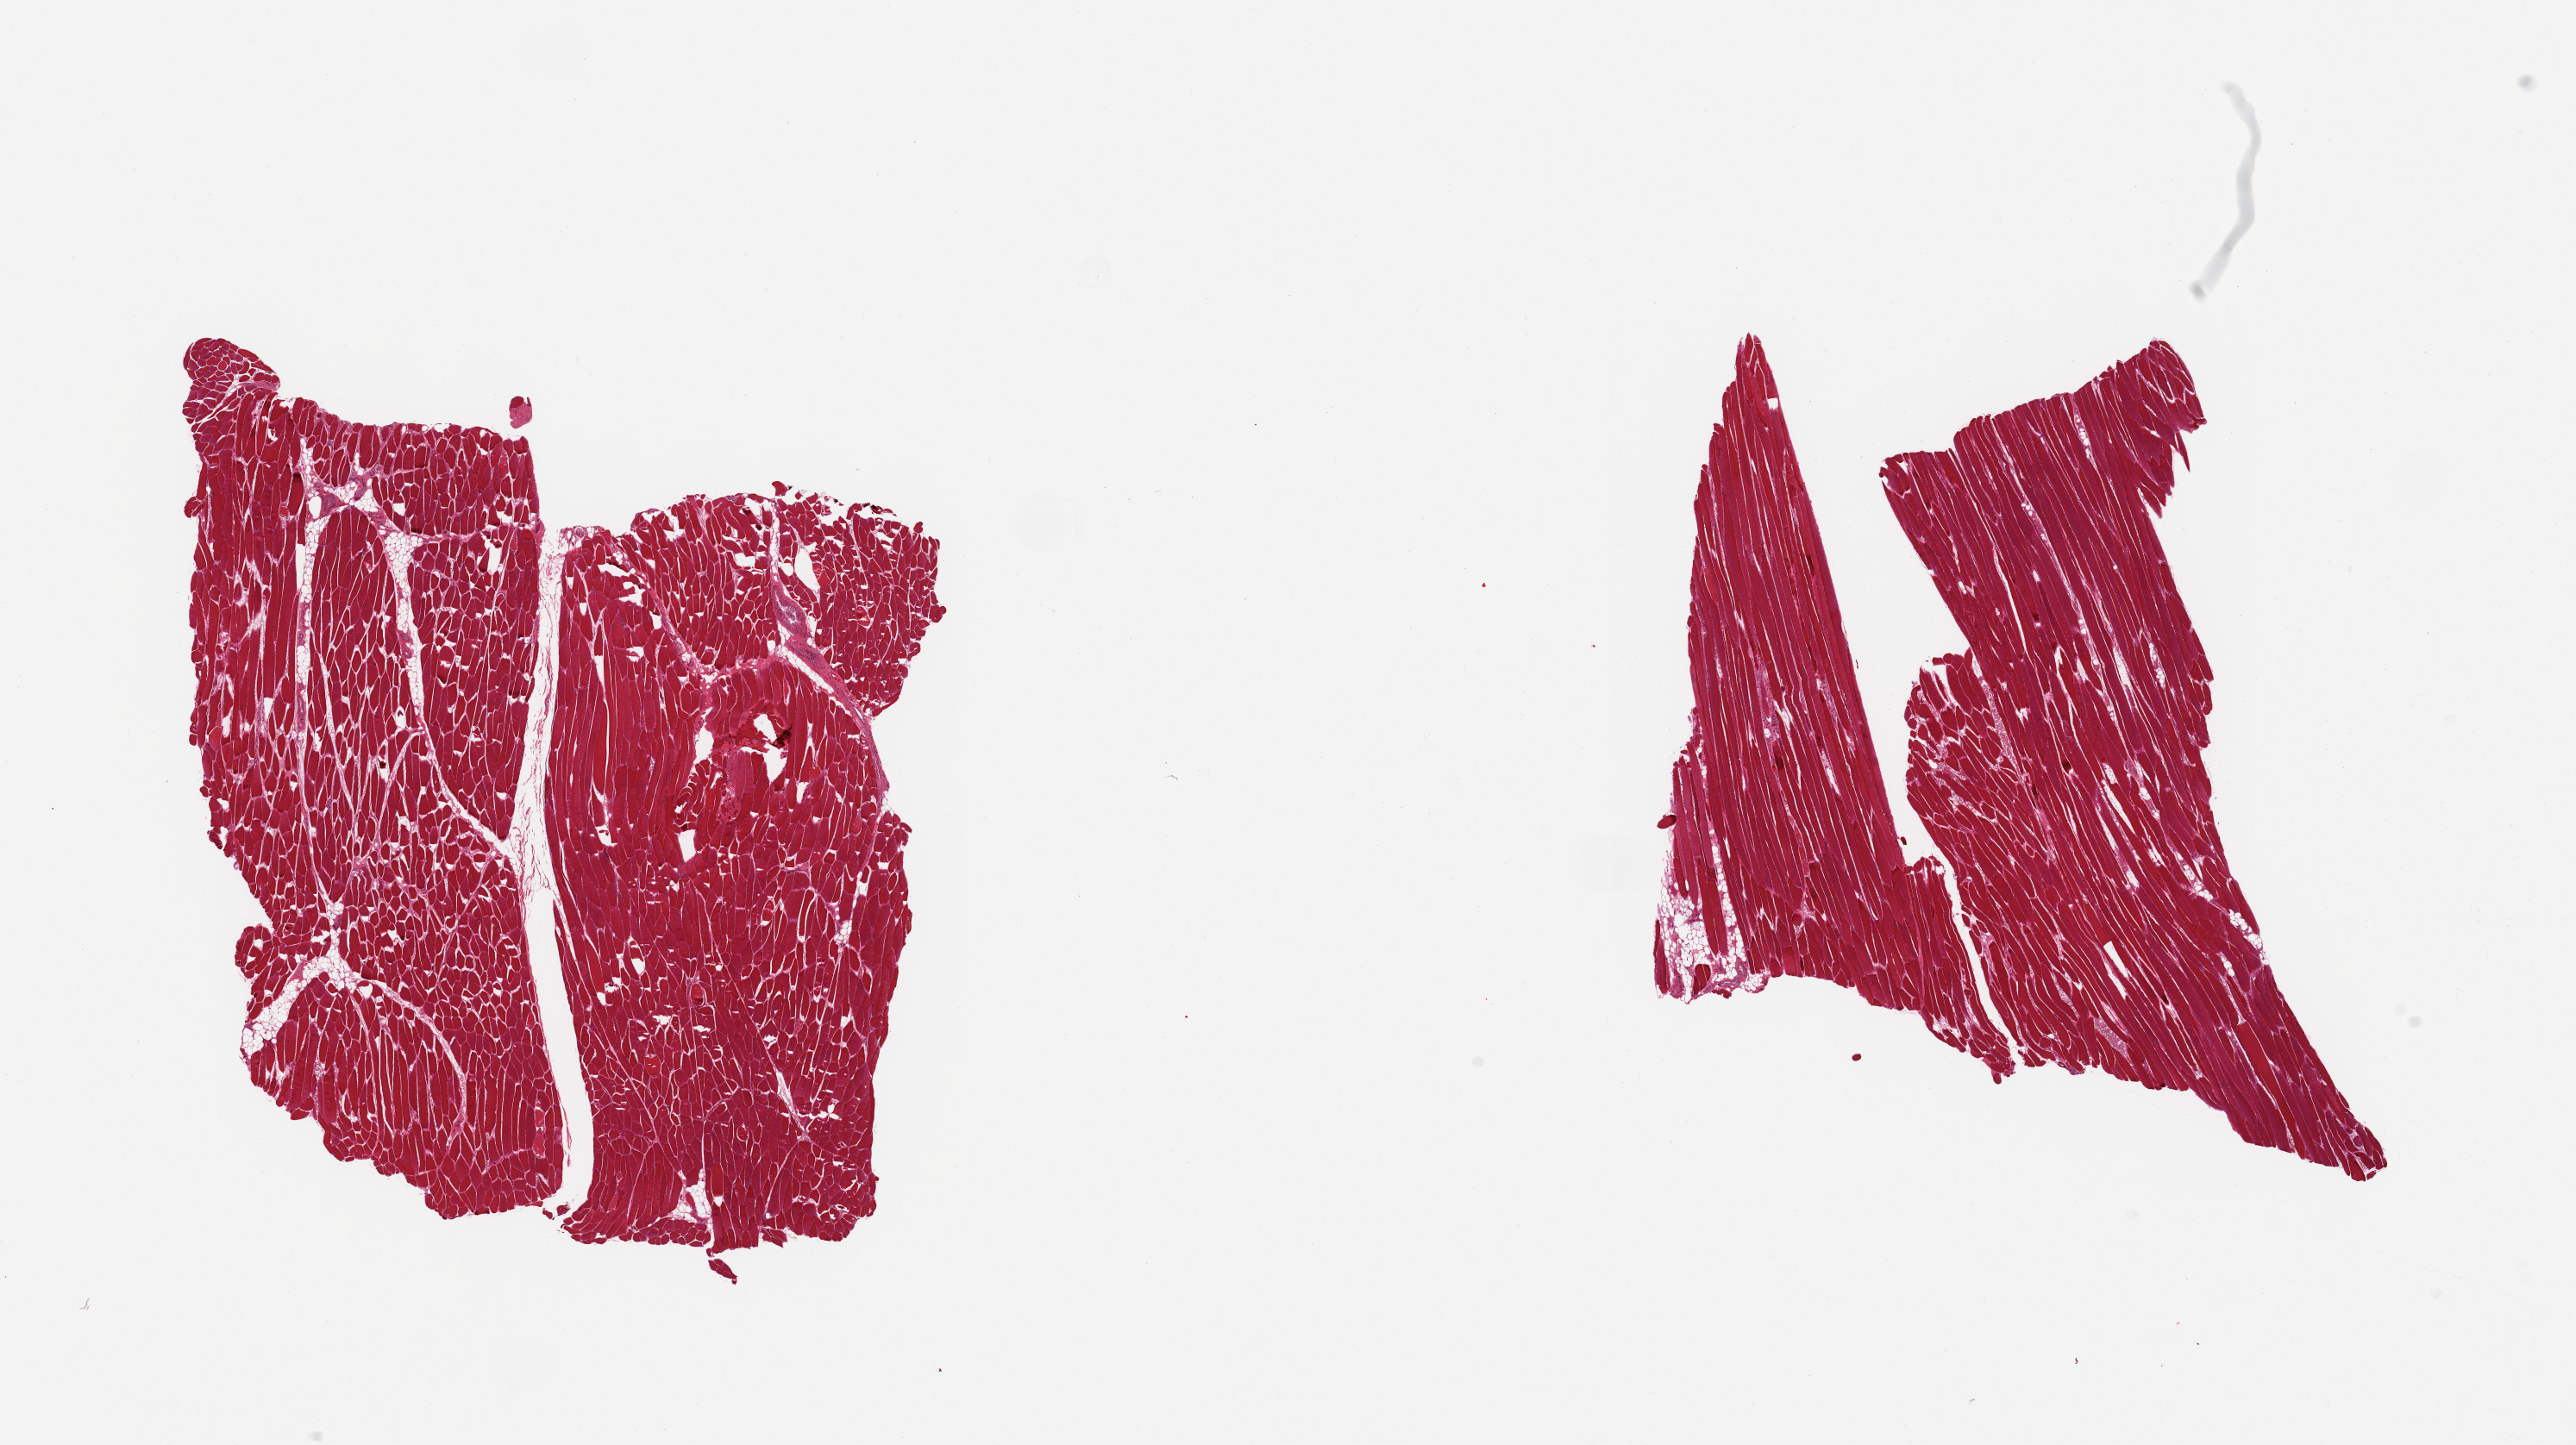
H&E whole-slide image, a low-resolution overview of the entire scanned area, about 23.6 x 13.3 mm. PAXgene-fixed paraffin-embedded (PFPE) section. Section of skeletal muscle (target tissue). Tissue donor sample.
- reviewer comment on this tissue sample: 2 pieces, ~5% interstitial fat